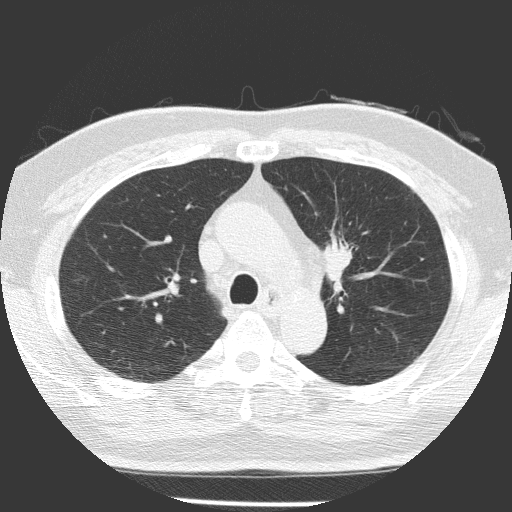
Low-dose screening chest CT, one axial slice; reconstruction kernel FC51; lung window (W 1500 / L -600 HU); 2 mm slice thickness; 512 × 512 image matrix.
Structures marked on this image (outlined manually by an expert reader):
- lesion 1 (tumor, upper lobe of left lung): bounding box [x1, y1, x2, y2] px = [323, 241, 352, 276]